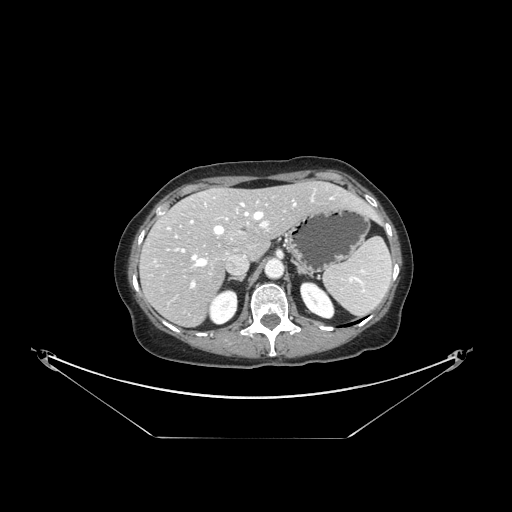
Contrast-enhanced abdominal CT, one axial slice. Soft-tissue window (W 400 / L 40 HU). 2.5 mm slice thickness. 512 × 512 image matrix, field of view 500 × 500 mm. Female patient, age 73 years. From the clinical record (not read from this slice): diagnosis: colorectal cancer liver metastases, imaged before liver resection; multiple liver metastases: no; largest metastasis: 1 cm; disease in both lobes: no.
Structures marked on this image (manually delineated by an expert):
- hepatic veins: bounding box <168,197,334,266> (left, top, right, bottom; pixels)
- liver: <142,182,372,326>
- planned liver remnant (the part of the liver to remain after resection): <168,182,371,257>
- portal vein (with intrahepatic branches): <175,204,268,288>